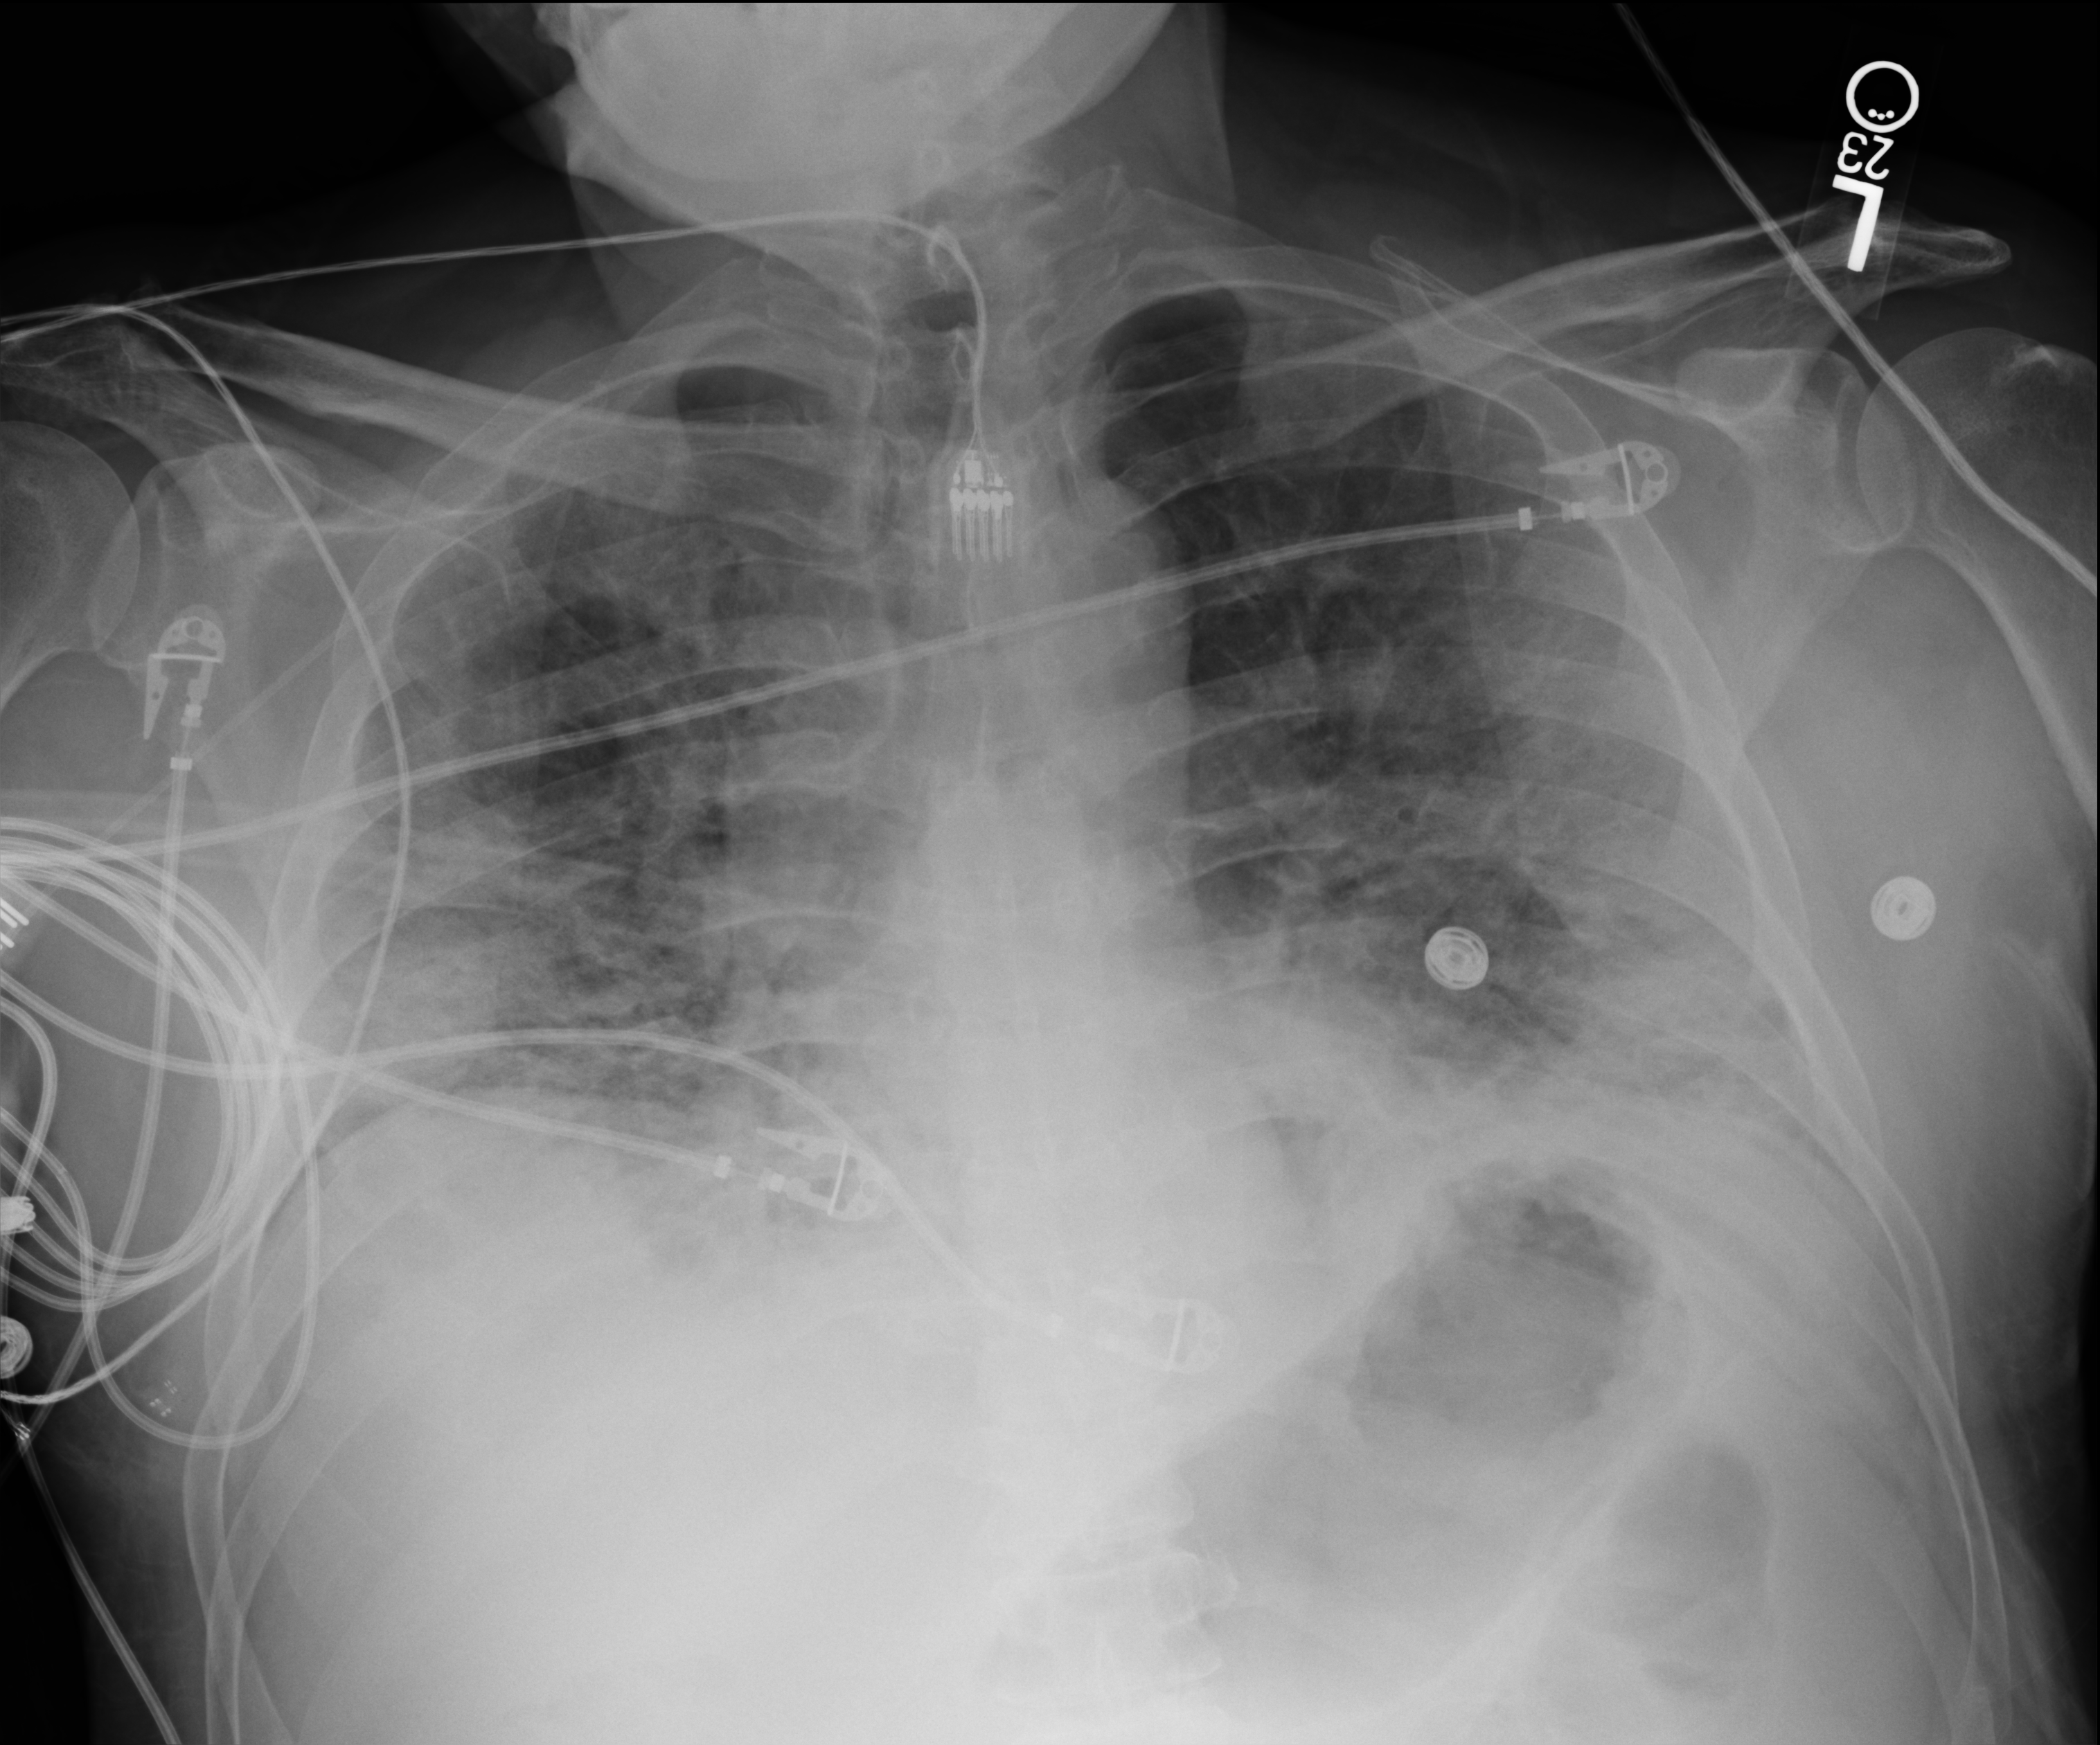
Bedside chest radiograph (computed radiography), anteroposterior (AP) projection. Male patient hospitalised with COVID-19, age 18–59 years.
From the hospital-stay record, not from the radiograph (when in the stay this image was taken is not recorded):
- other chronic lung disease (admission record): no